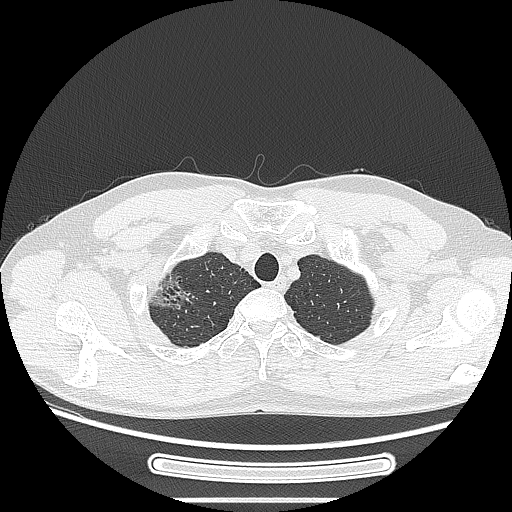
Chest CT, one axial slice. Slice 233 of 269 in the series (ordered by position). Reconstruction kernel LUNG. 120 kVp. Lung window (W 1500 / L -600 HU). 1.25 mm slice thickness. 512 × 512 image matrix, field of view 382 × 382 mm. Patient: male, 53 years. Case-level facts recorded for this patient, not image findings: clinical TNM (as recorded): T1c N0 M0.
Structures marked on this image (rectangle marked by the reading radiologist):
- lung tumour (recorded histology: adenocarcinoma): box from (x=134, y=273) to (x=196, y=318) px